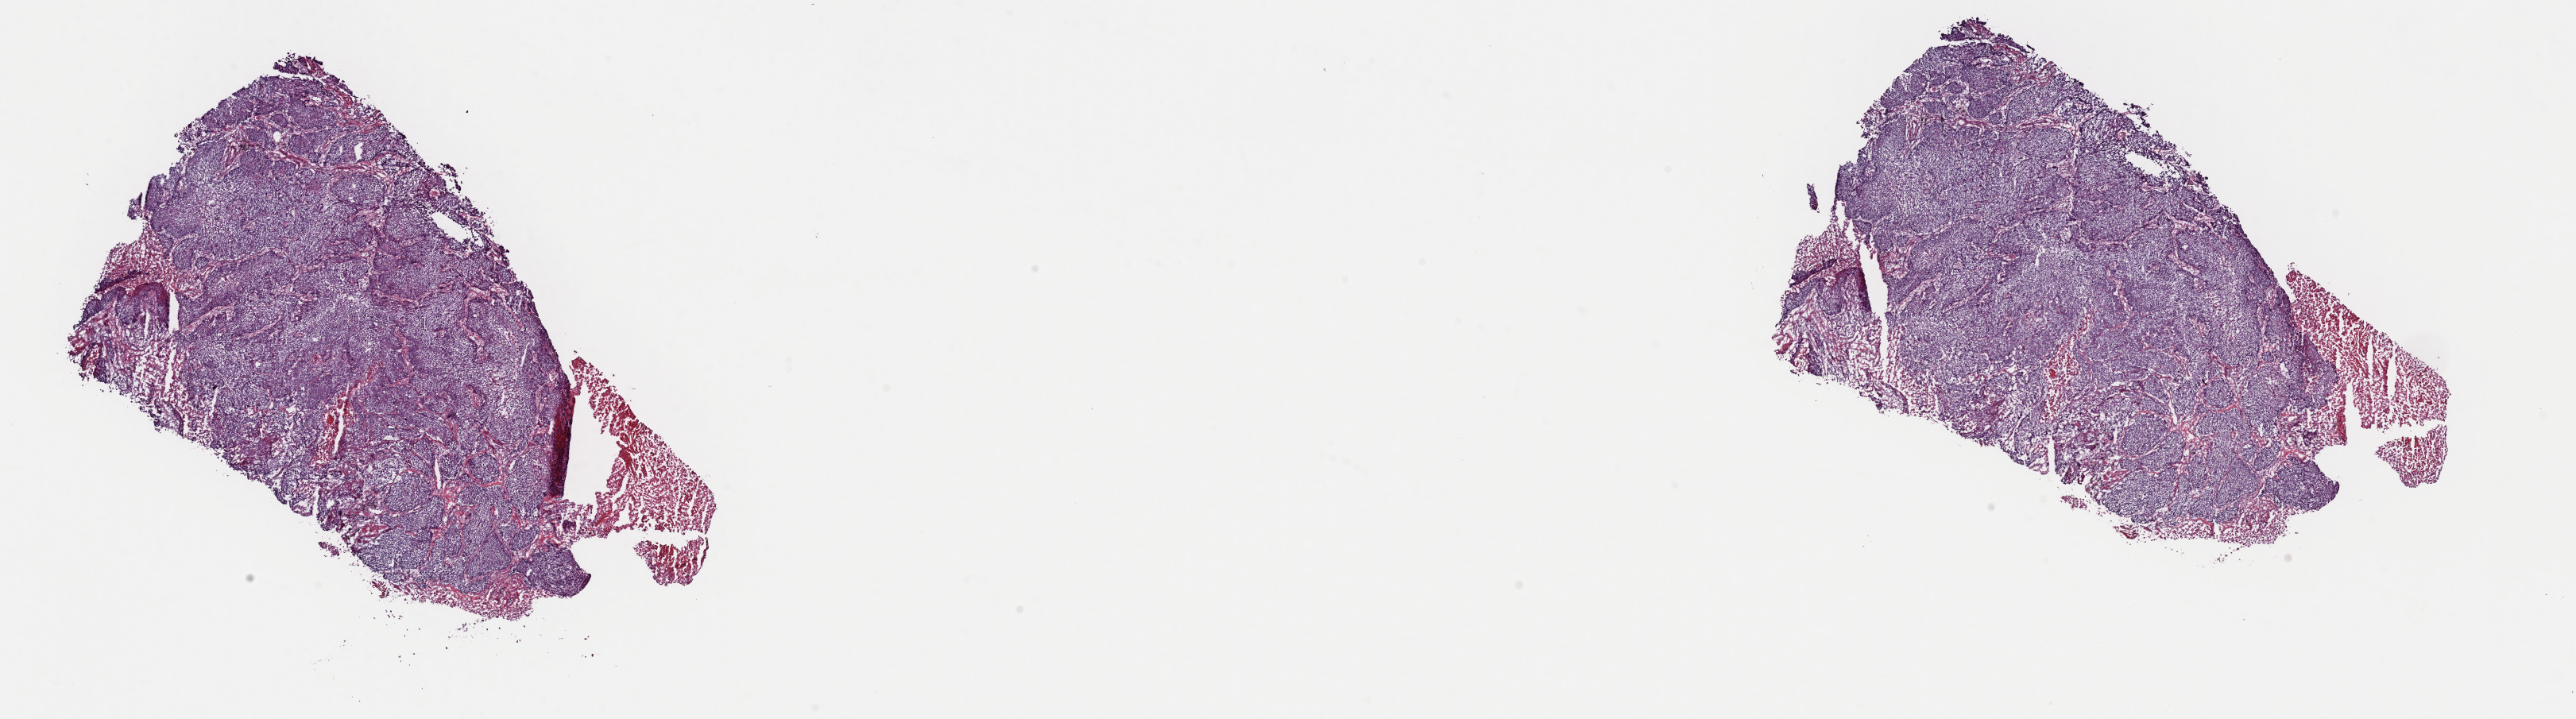
Digitized Hematoxylin and eosin (H&E) stained tissue section (whole slide), low-resolution overview of the scanned area, about 25.6 x 7.1 mm (acquisition: 40x scan). Frozen section from the top of the tissue portion. Lung, primary tumour sample. Patient: male, age at initial diagnosis 67 years. Pathologist review of this section (percent, as recorded): tumour cells 80%, tumour nuclei 80%, normal cells 5%, stromal cells 10%, necrosis 5%. Infiltration values recorded for this section: lymphocyte infiltration 70%, monocyte infiltration 15%, neutrophil infiltration 5%.
- pathologic diagnosis: Squamous cell carcinoma, NOS (lower lobe, lung)
- laterality: right
- AJCC pathologic stage: IIA